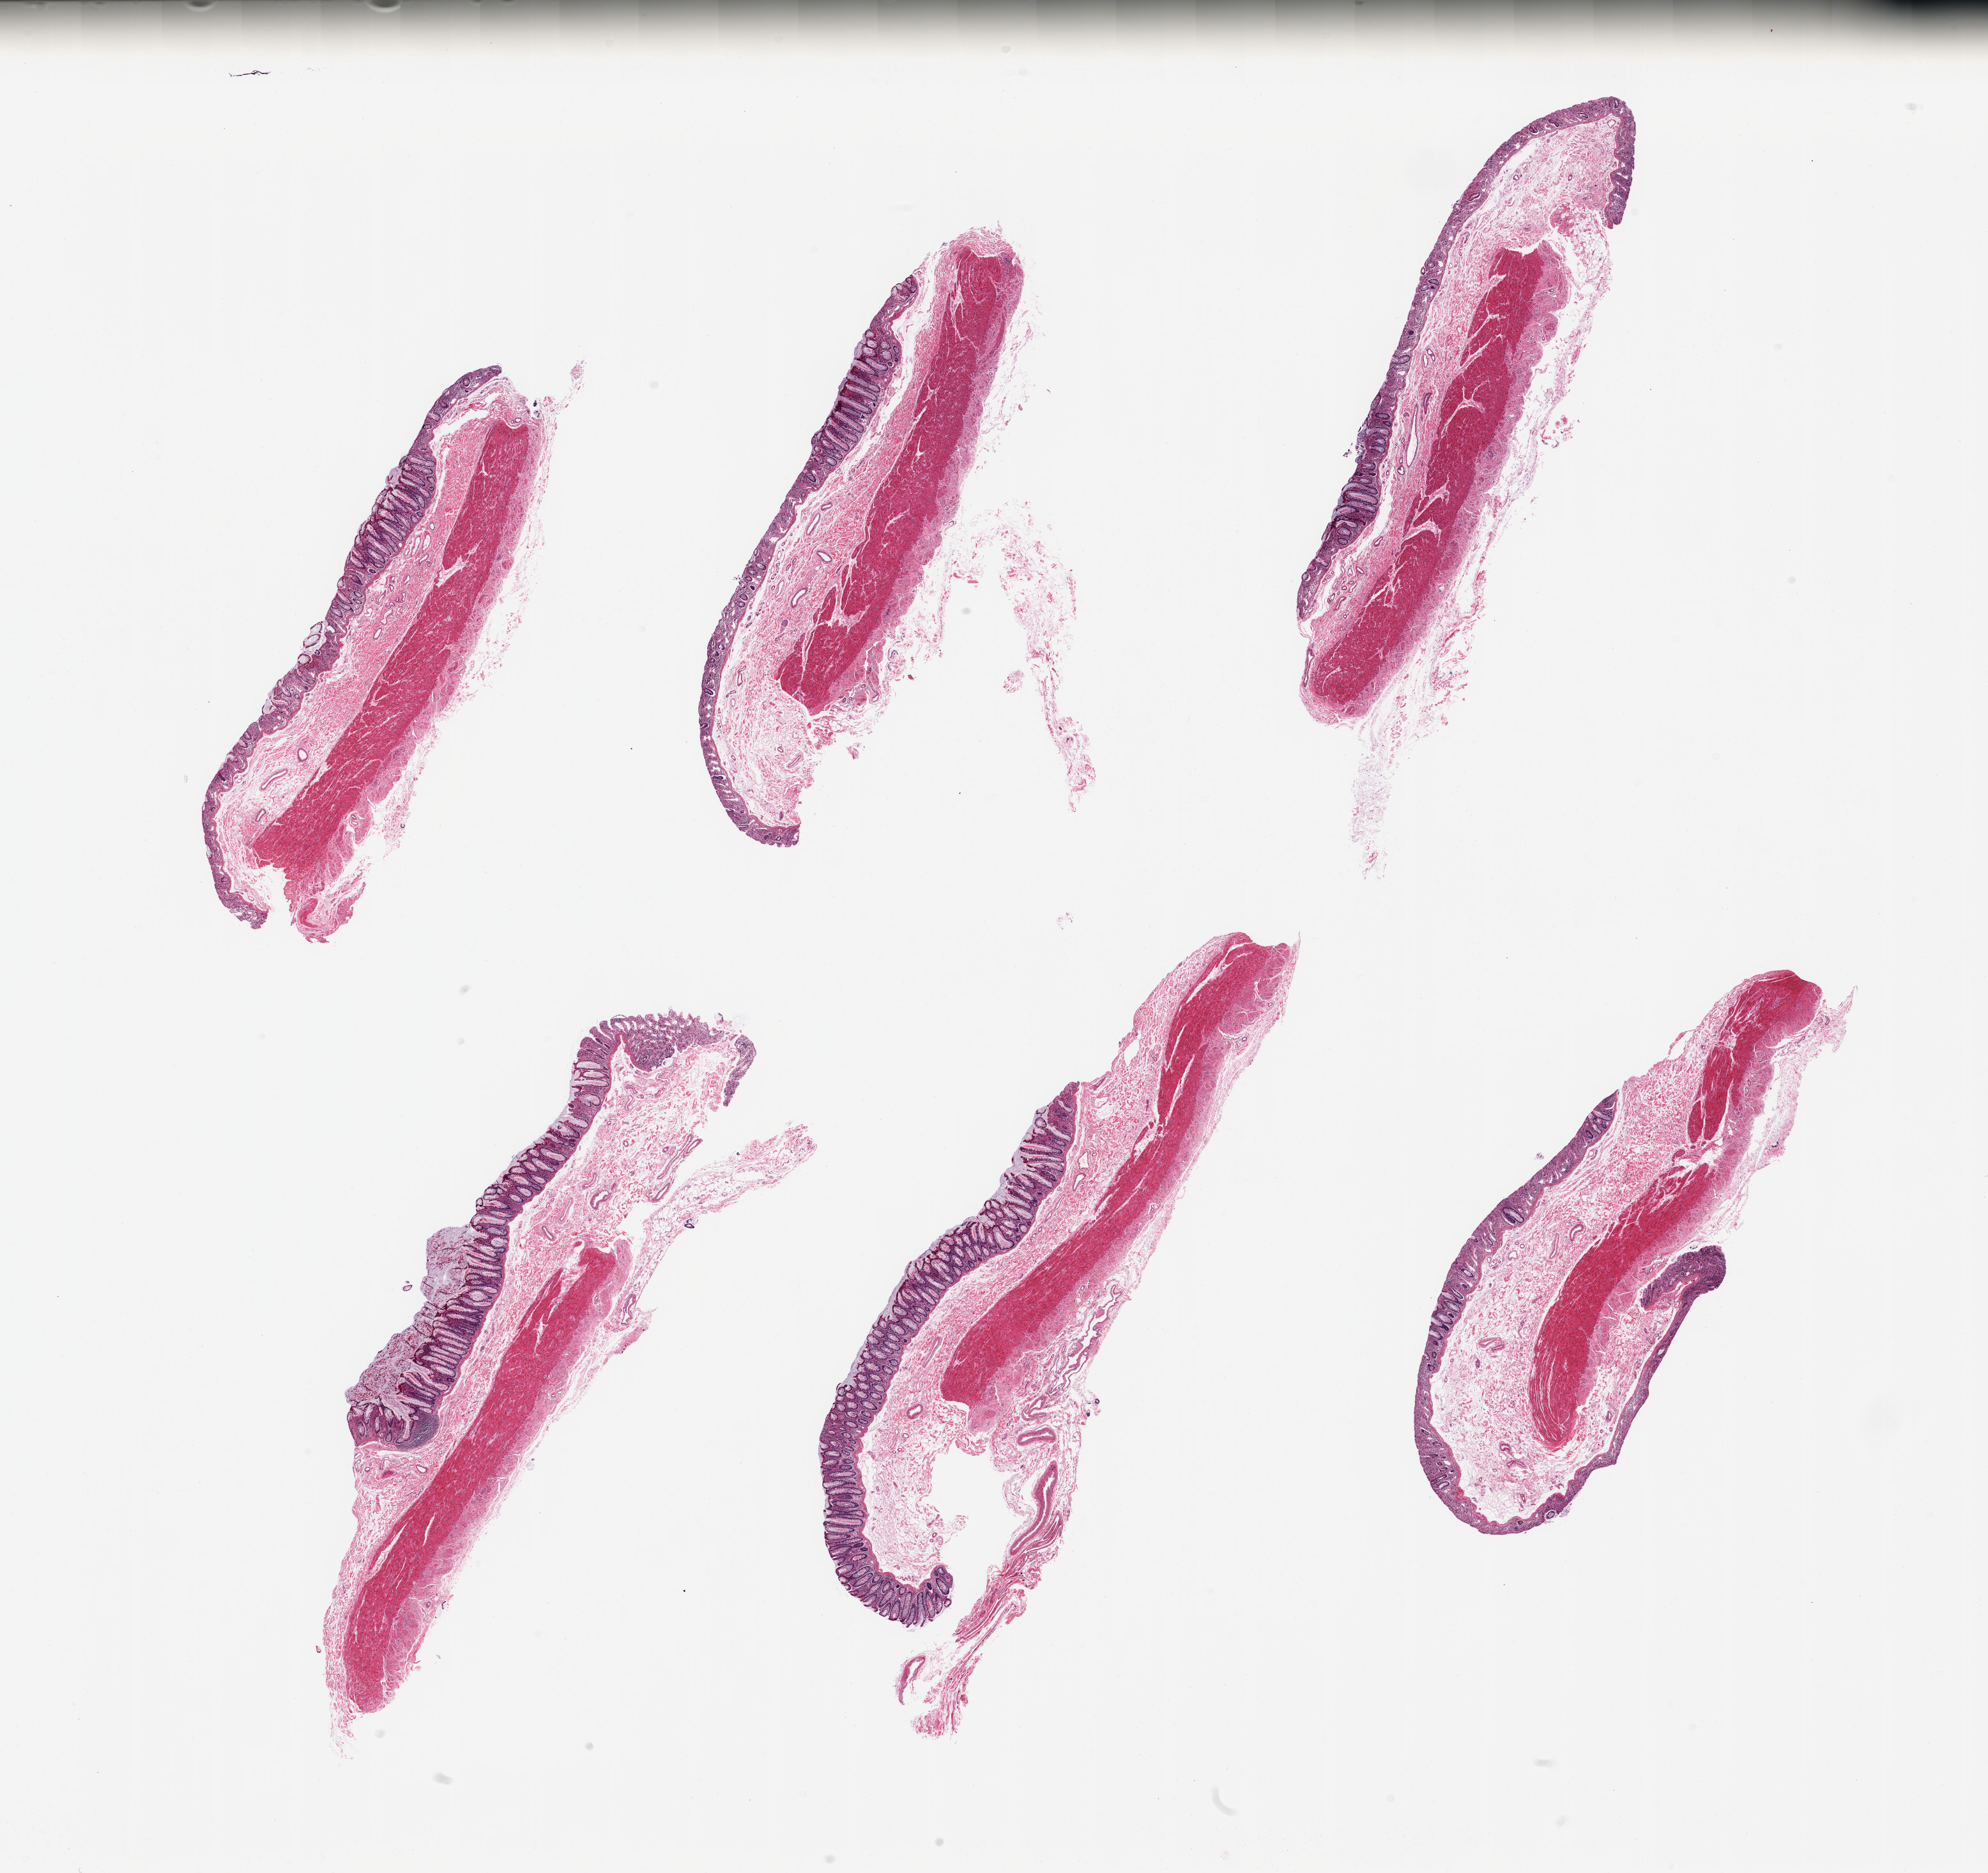
Haematoxylin and eosin whole-slide image, brightfield, a low-resolution overview of the entire scanned area, about 24.6 x 23.2 mm (from a 20x scan). PAXgene-fixed paraffin-embedded (PFPE) section. Sampled site (target tissue): transverse colon. Tissue donor sample. Male donor.
Pathologist's review note for this sample: 6 pieces, mucosa up to ~0.5mm-variably fixed, mainly score 1, focal areas score 2 with gland sloughing.